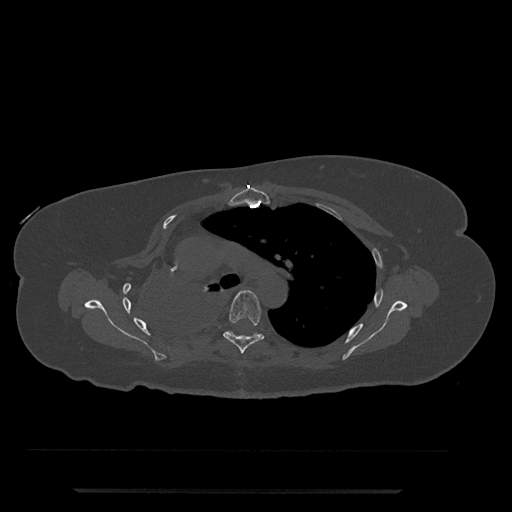
CT including the spine, one axial slice; position 540 of 797 along the scan axis; bone window (W 1800 / L 400 HU); 0.5 mm slice thickness; 512 × 512 image matrix, field of view 440 × 440 mm. Patient: female, 51 years. Case-level facts recorded for this patient, not image findings: primary cancer: neuro.
Outlined on this slice (semi-automatically segmented with operator editing):
- T5 vertebra: bounding box (x1, y1, x2, y2) in pixels: (223, 290, 265, 354)
- T6 vertebra: (226, 331, 257, 335)